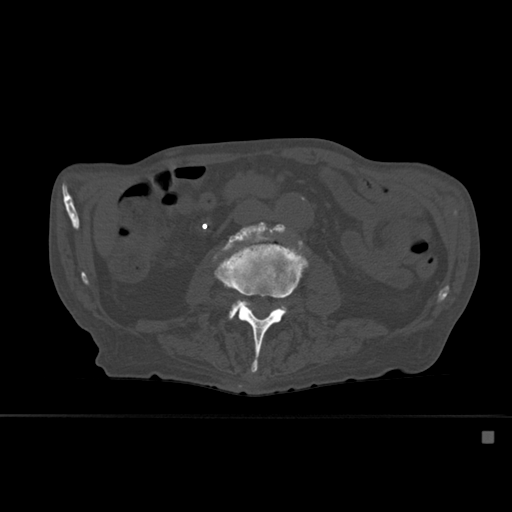
CT including the spine, one axial slice. Slice 211 of 527 in the series (ordered by position). Bone window (W 1800 / L 400 HU). 512 × 512 image matrix, field of view 373 × 373 mm. Male patient, age 78 years. Case-level facts recorded for this patient, not image findings: primary cancer: prostate.
Structures marked on this image (semi-automatically segmented with operator editing):
- L3 vertebra: bounding box <212,229,309,372> (left, top, right, bottom; pixels)
- L4 vertebra: <223,227,290,320>